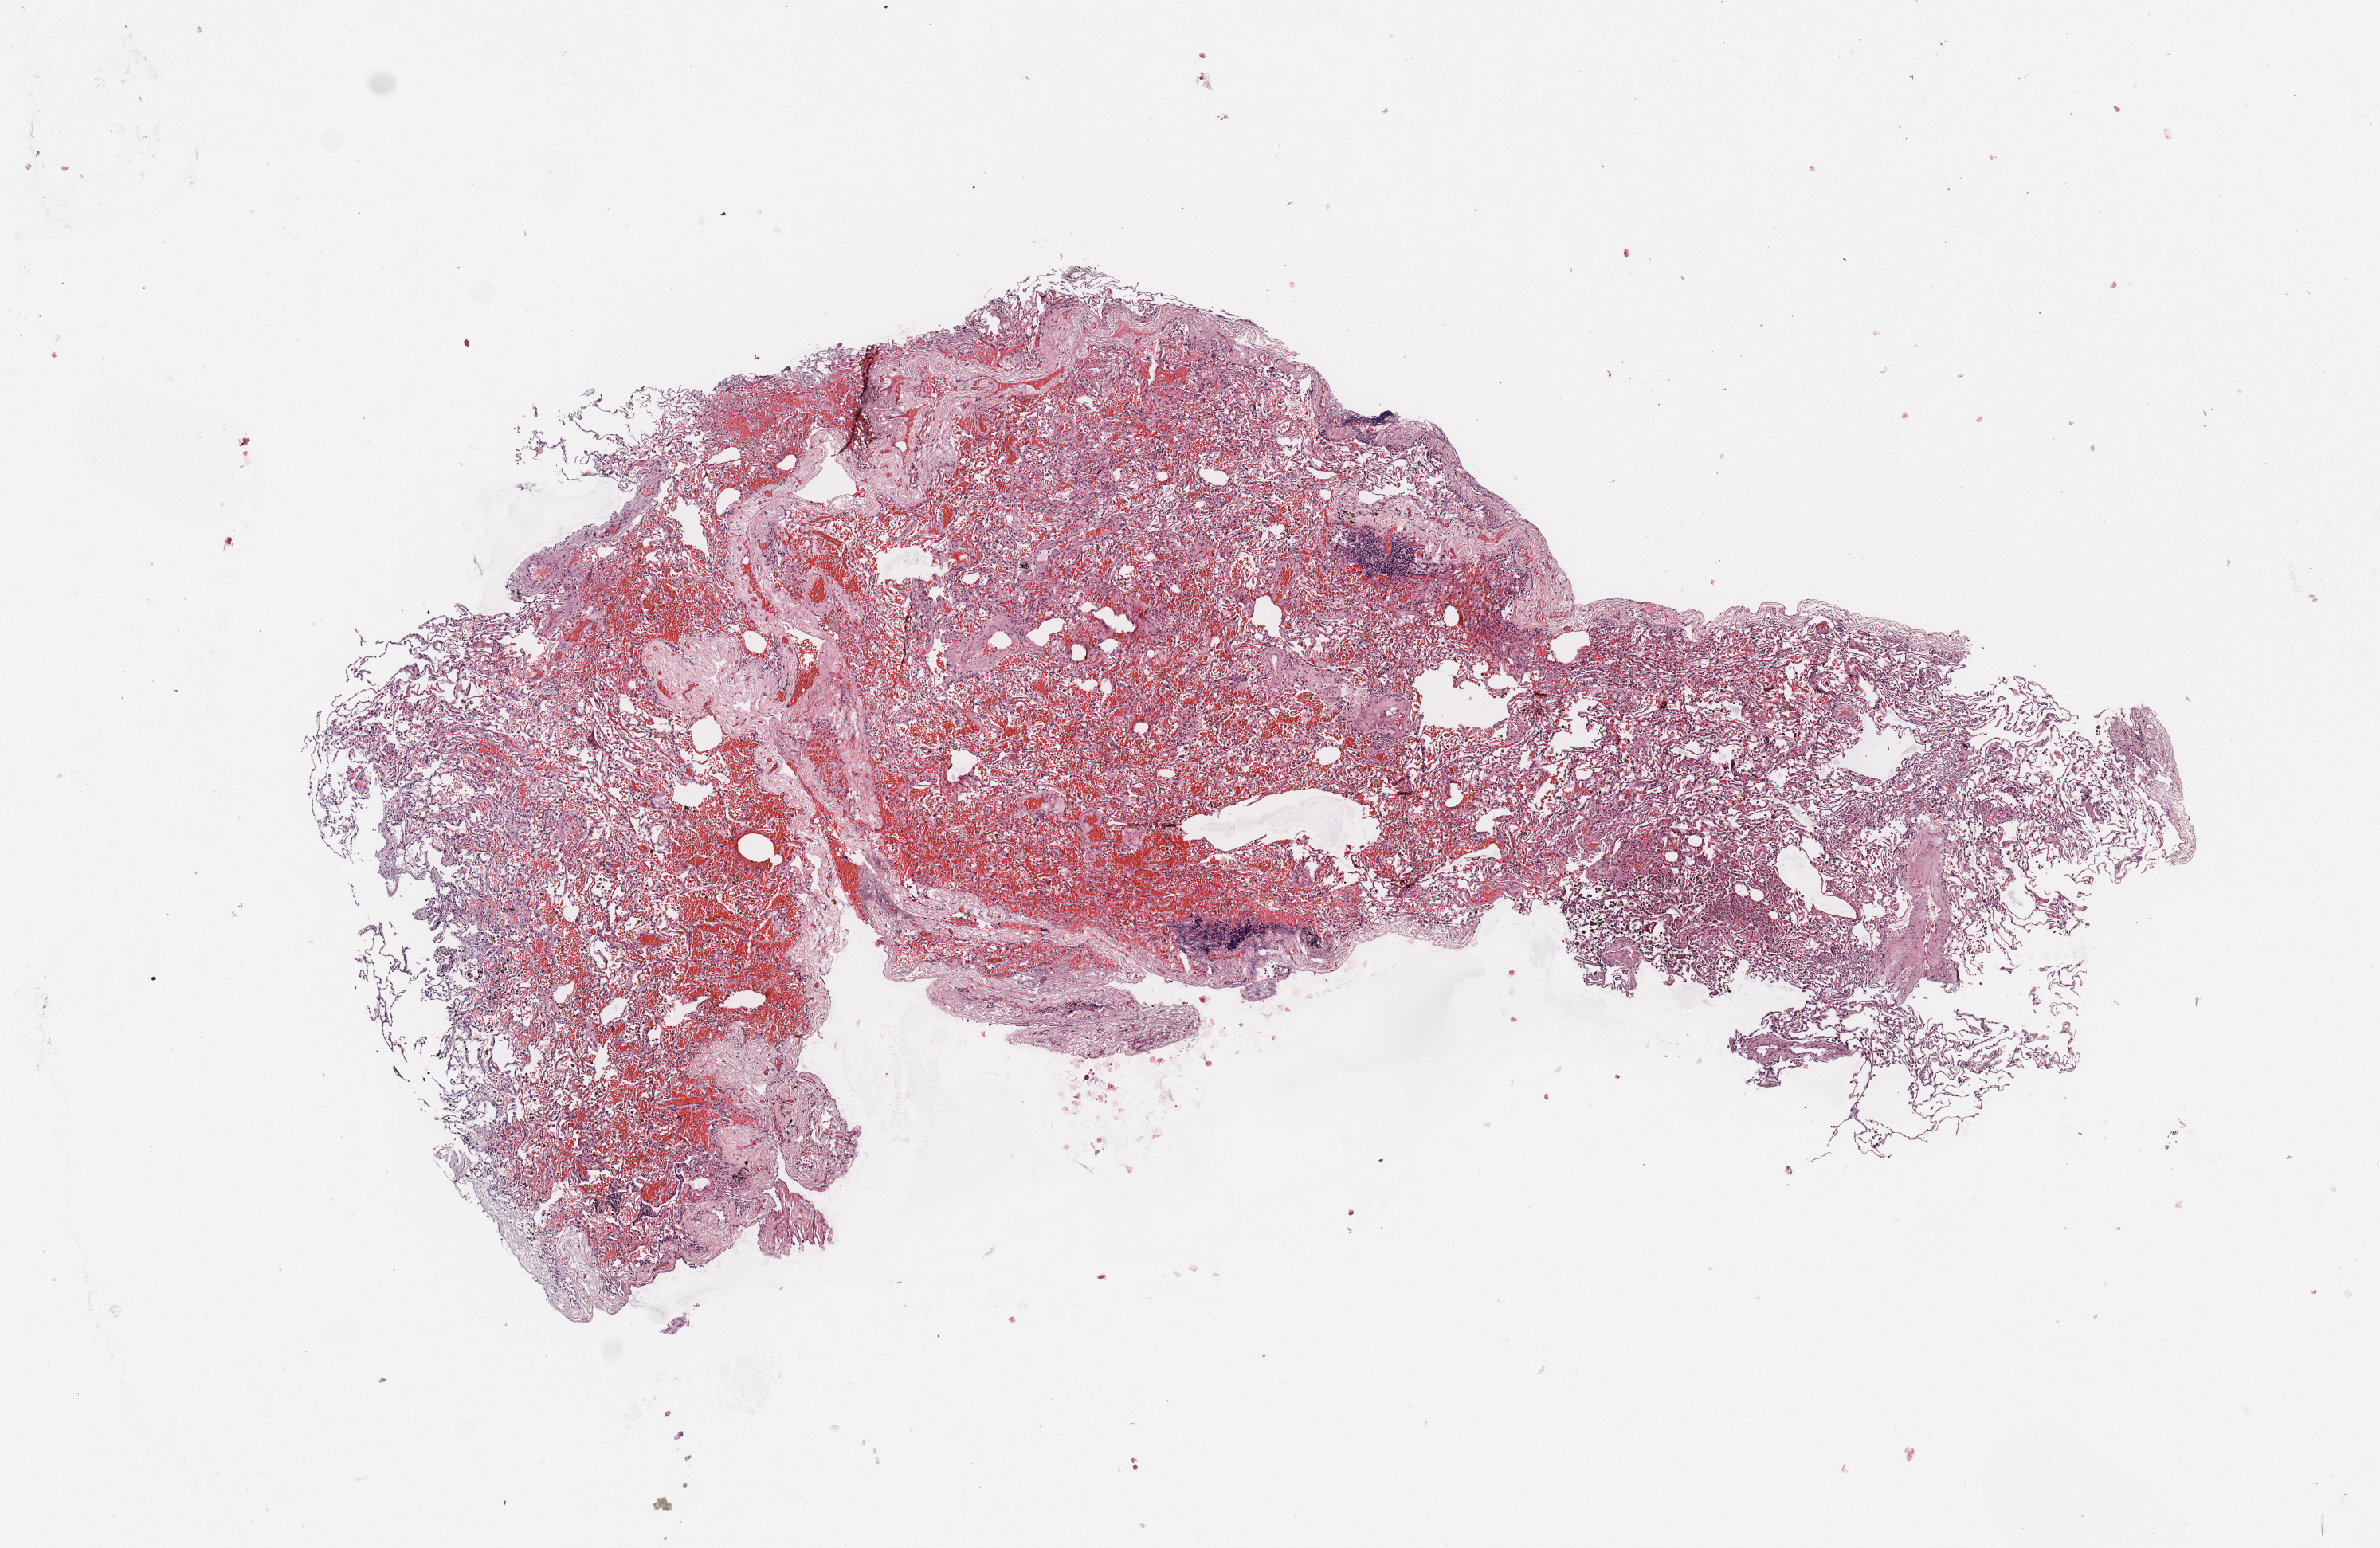
Digitized H&E-stained tissue section (whole slide) — a low-resolution overview of the entire scanned area, about 11.8 x 7.7 mm (acquisition: 20x scan), normal (non-tumour) tissue sample, sampled site: lung. Male, 64 y/o.
- this section: normal (non-tumour) tissue from the same patient
- patient diagnosis: Adenocarcinoma, NOS